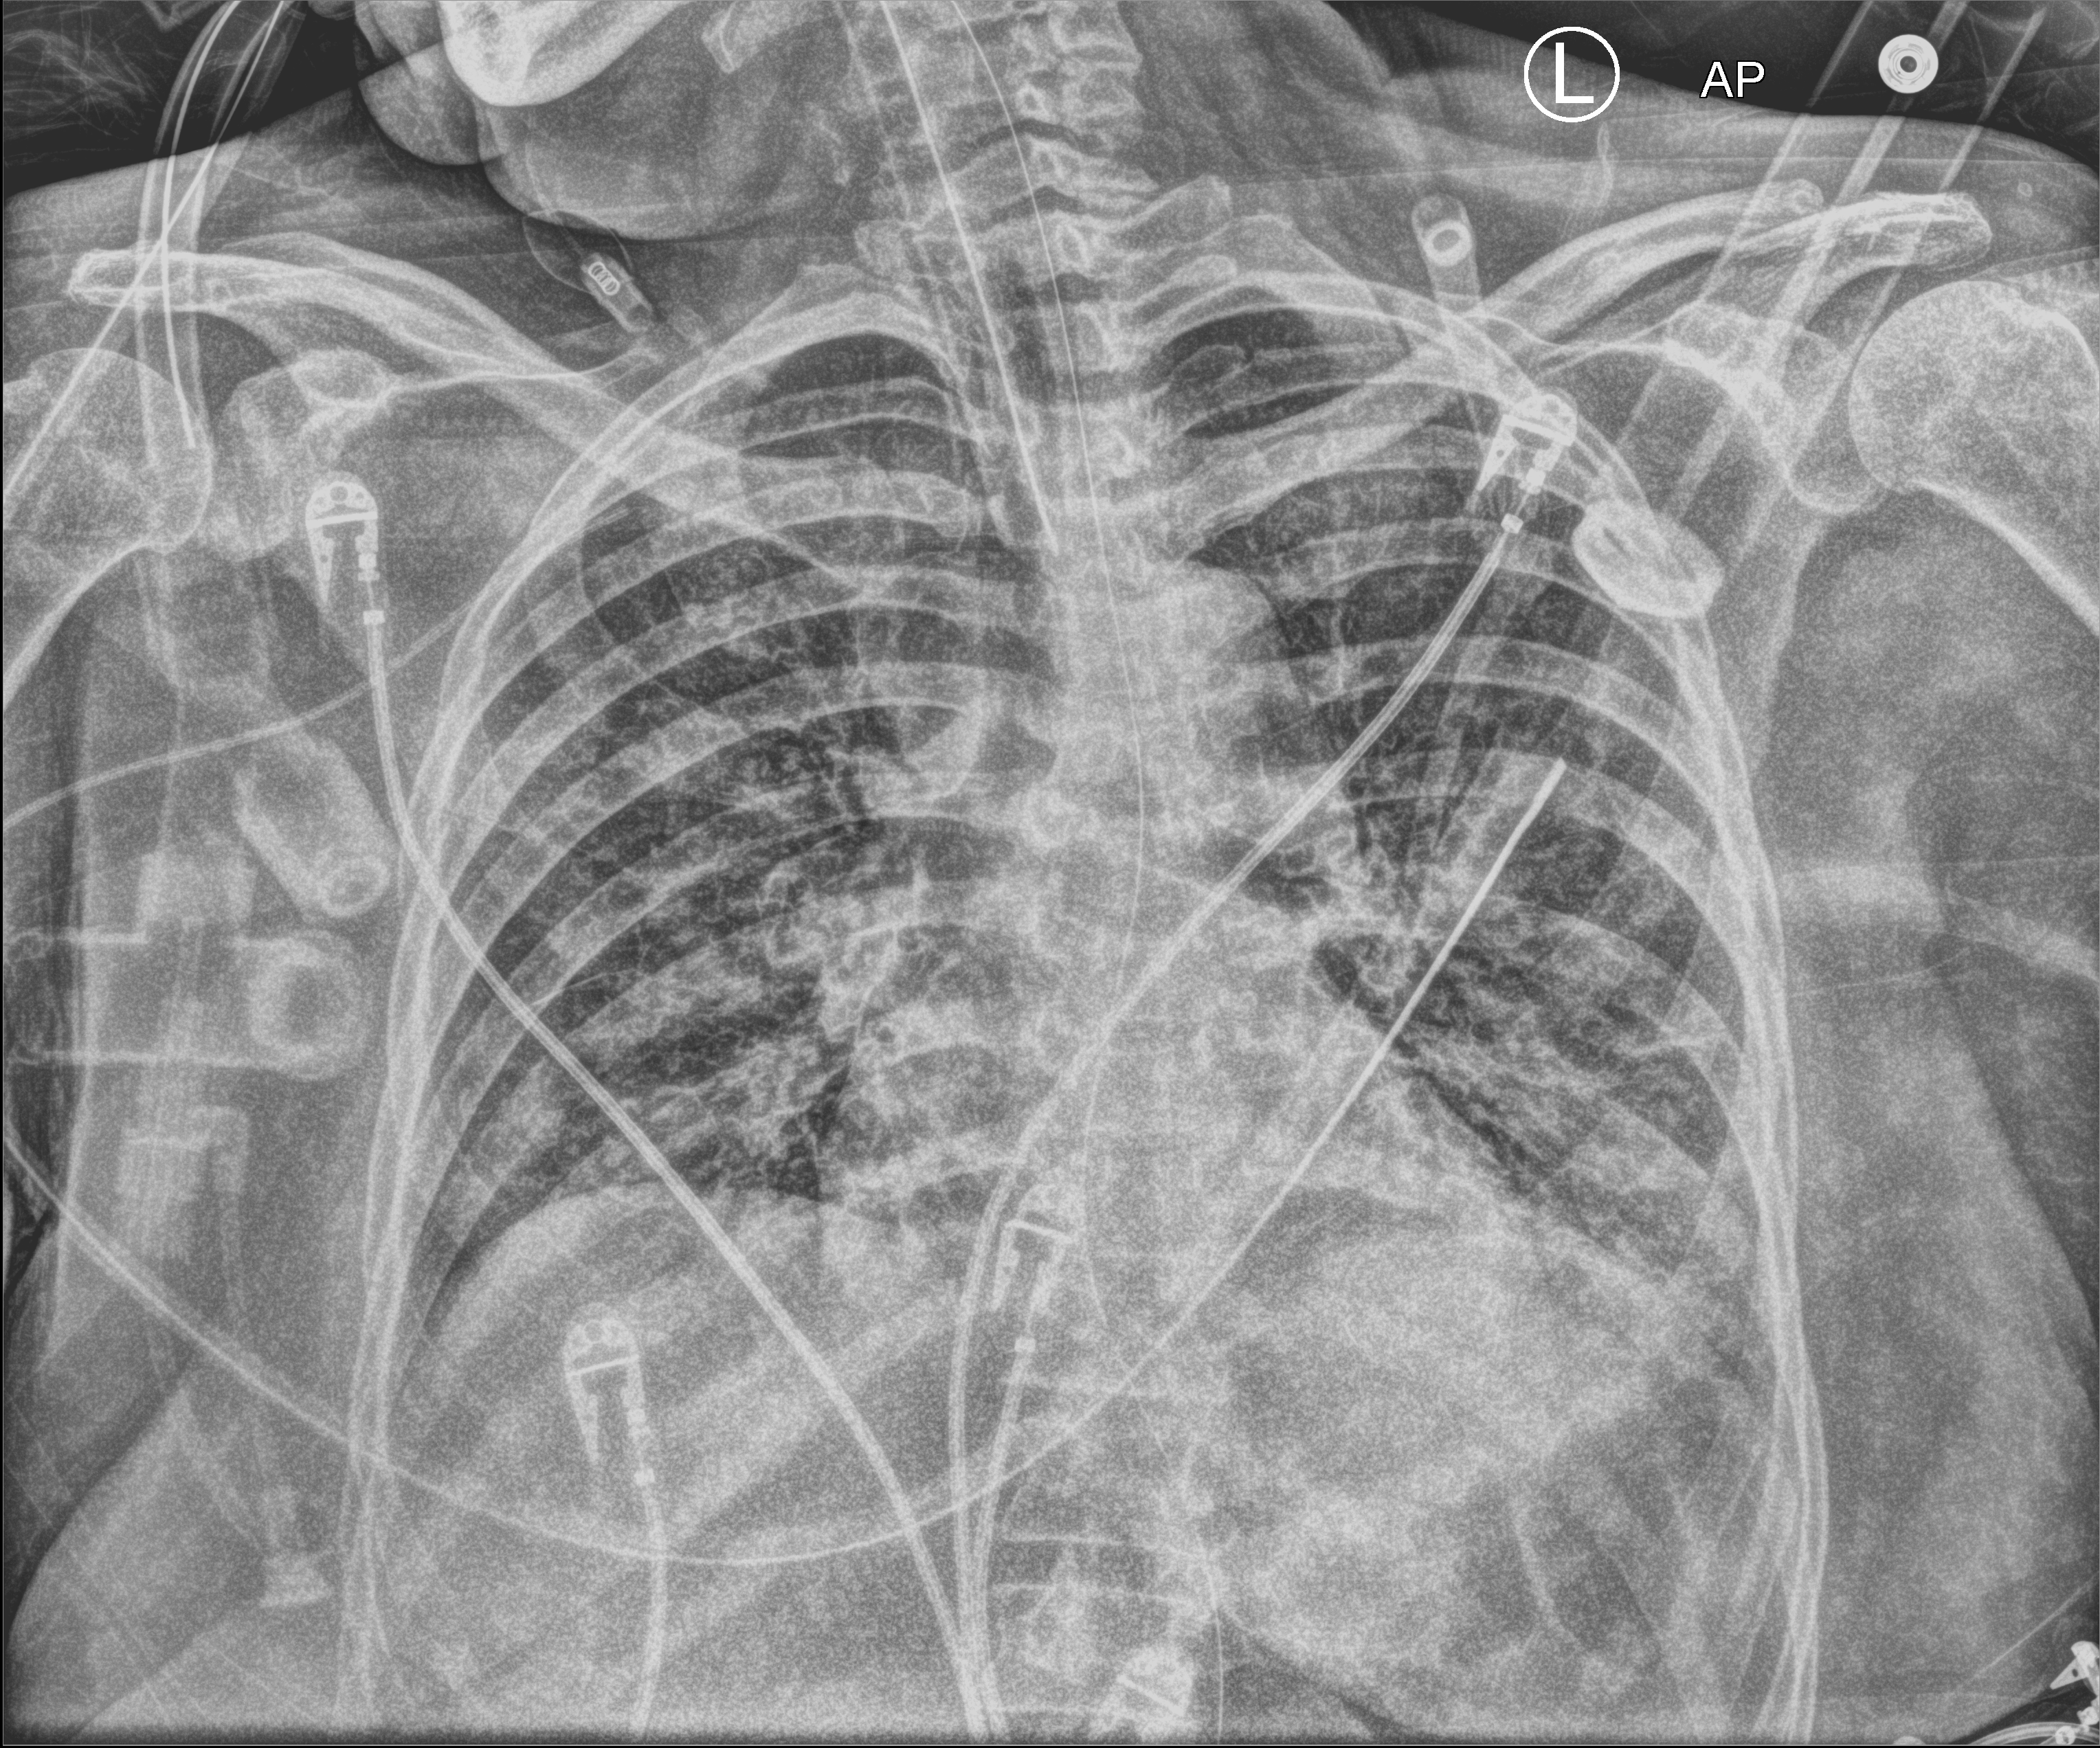
Chest X-ray (portable), anteroposterior (AP) projection. Patient hospitalised with COVID-19; female, aged 75–90 years.
Admission-level facts for this patient (not findings on this image; timing relative to this image not recorded):
- admitted to intensive care during this hospital stay: yes
- mechanically ventilated during this hospital stay: yes